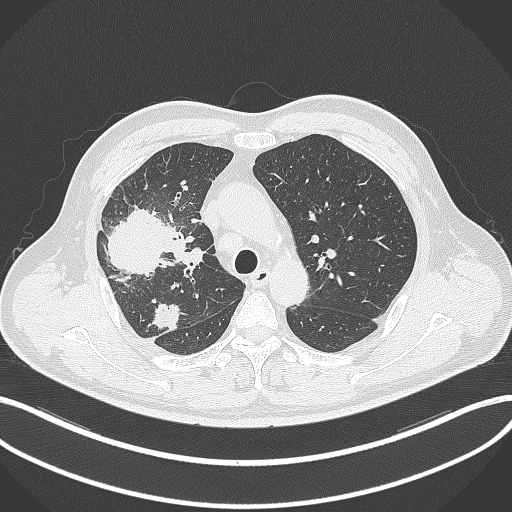
Chest CT, one axial slice; slice 234 of 348 in the series (ordered by position); lung window (W 1500 / L -600 HU); 1 mm slice thickness; 512 × 512 image matrix, field of view 400 × 400 mm. Male patient, age 55 years. From the clinical record (not read from this slice): clinical TNM (as recorded): T3 N2 M1.
Annotated regions visible in this slice (bounding box drawn by a radiologist):
- lung tumour (recorded histology: adenocarcinoma): bounding box <103,203,176,277> (left, top, right, bottom; pixels)